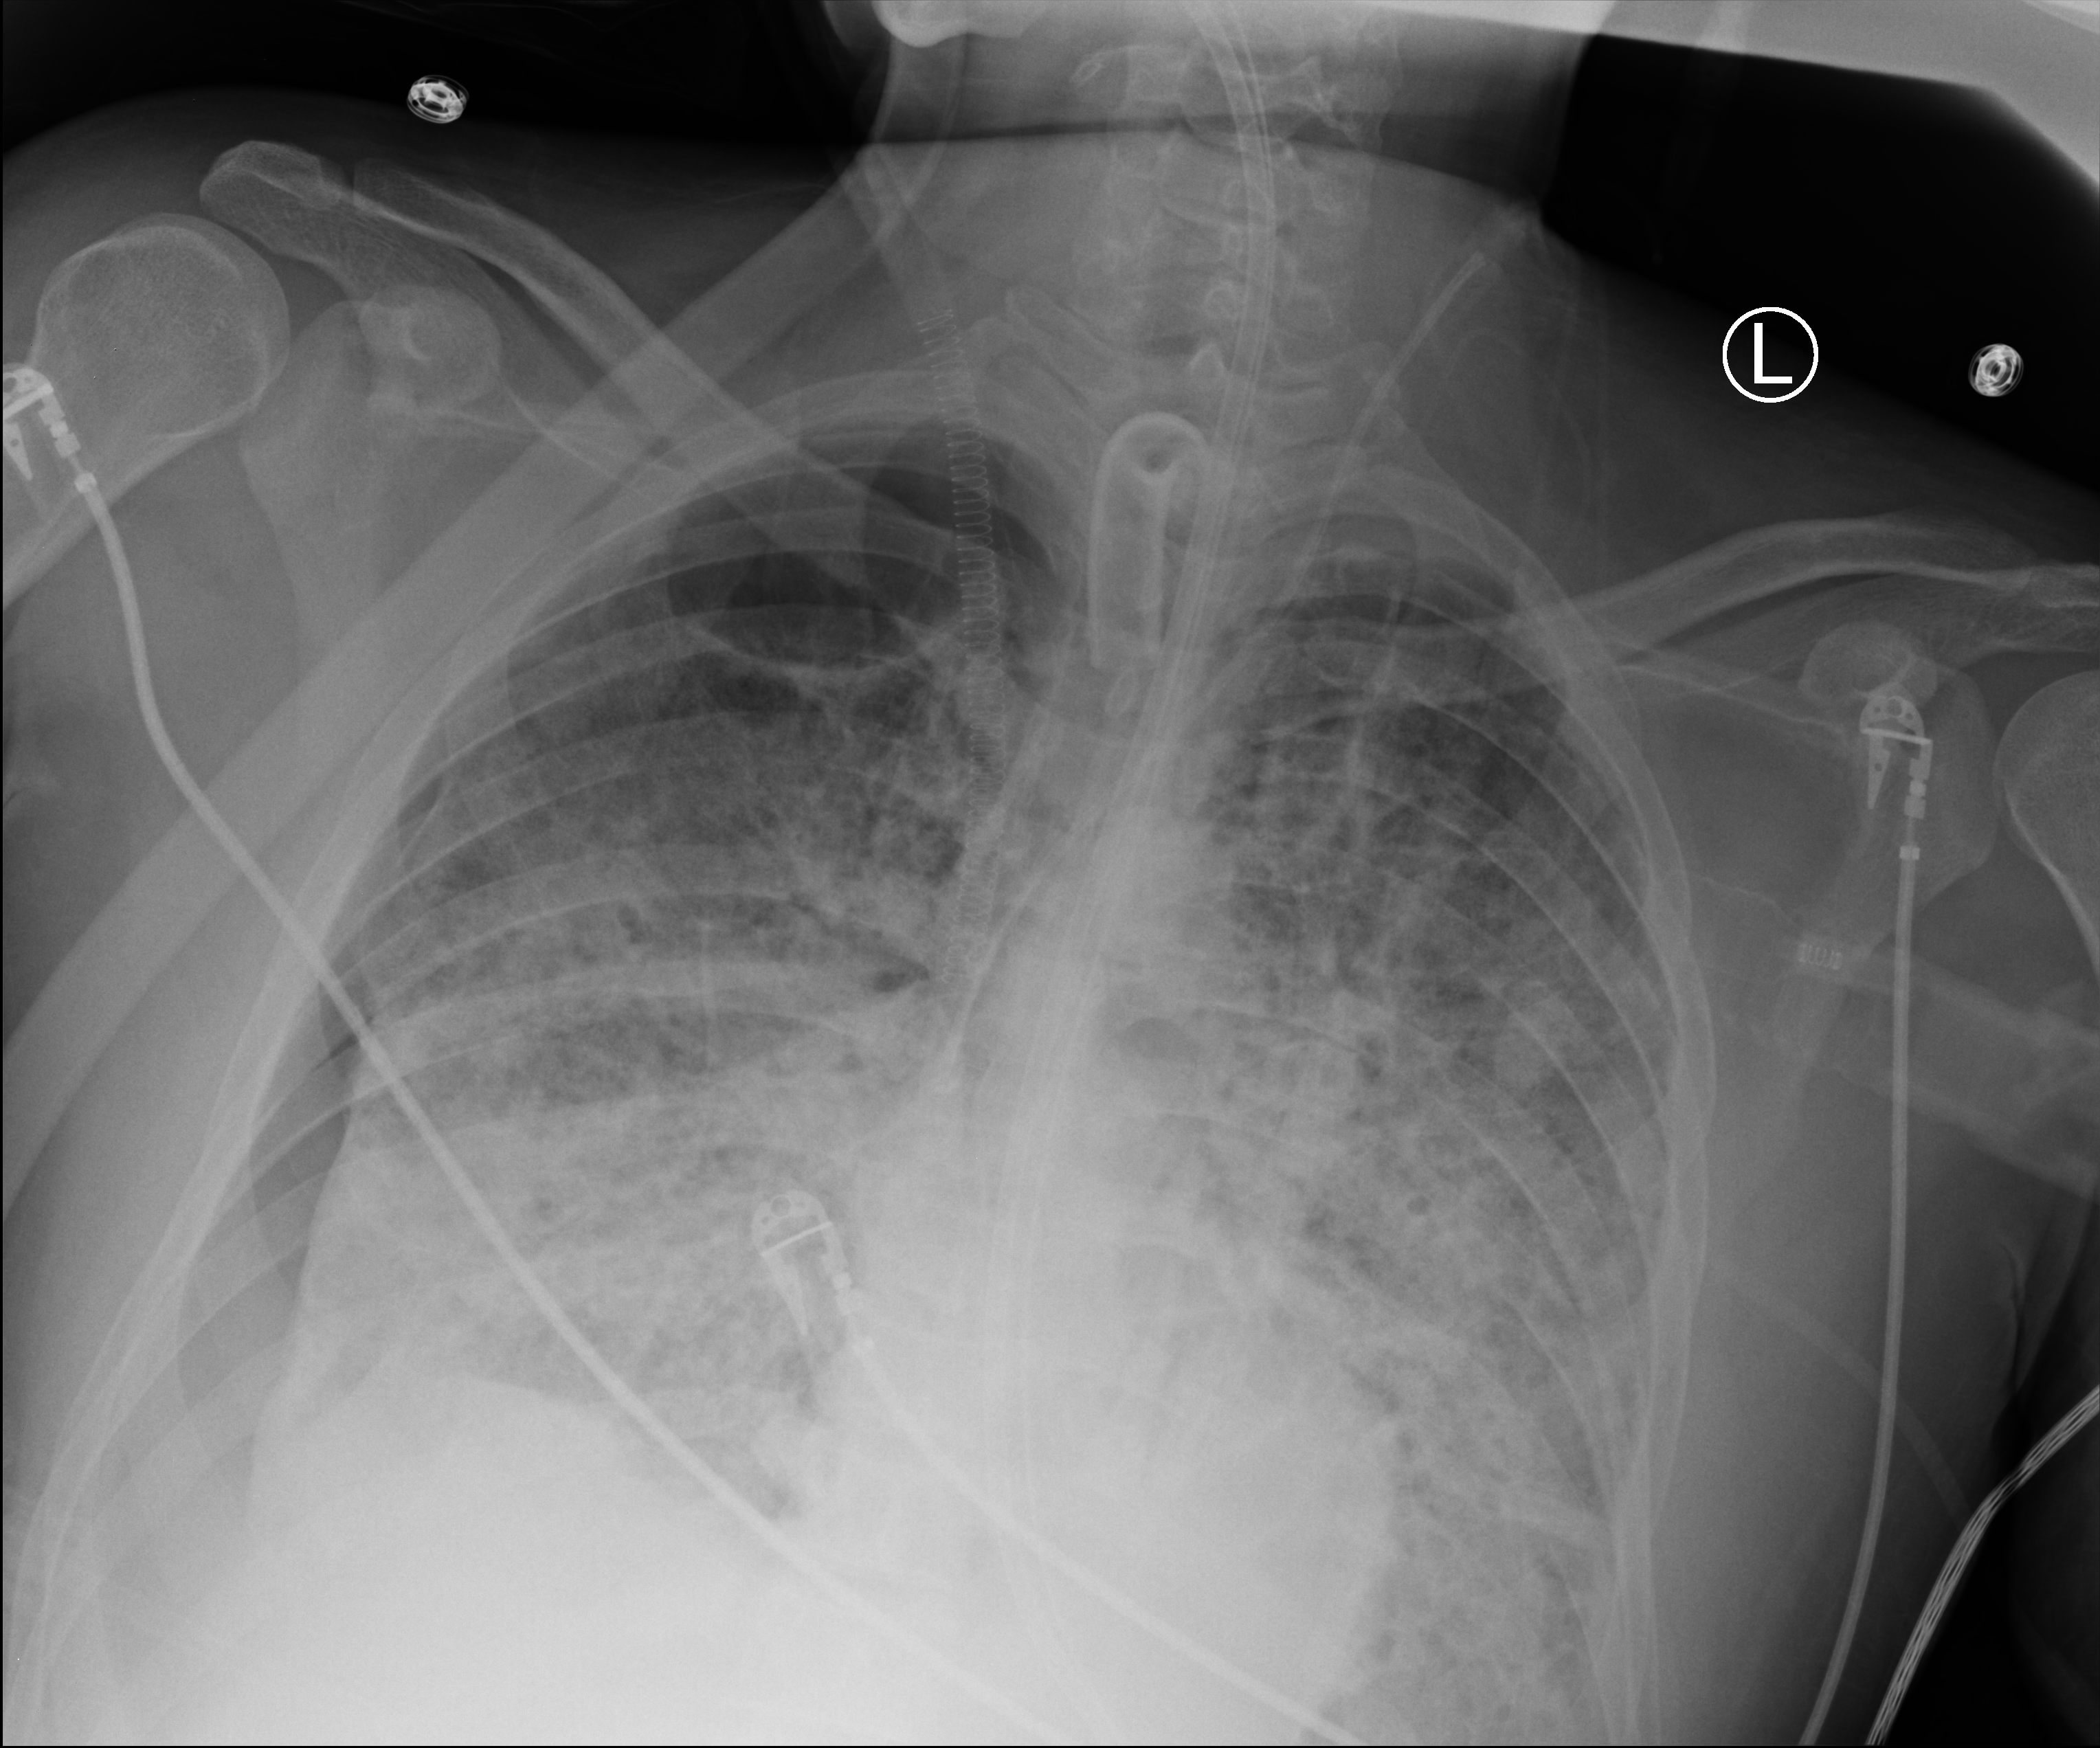
Bedside chest radiograph (computed radiography), anteroposterior (AP) projection. Adult patient hospitalised with COVID-19, age 18–59 years.
Admission-level facts for this patient (not findings on this image; timing relative to this image not recorded):
- admitted to intensive care during this hospital stay: yes
- COPD (admission record): no
- smoking status (admission record): never